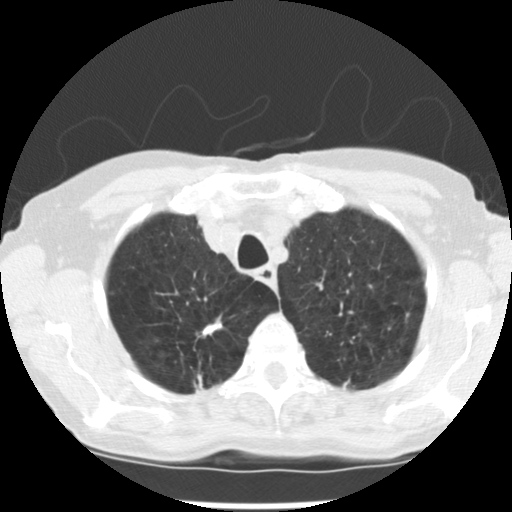
Low-dose screening chest CT, axial slice; first (baseline) screen; lung window (W 1500 / L -600 HU); 2.5 mm slice thickness; standard (soft-tissue) reconstruction kernel (STANDARD); 120 kVp; slice 39 of 265 in the series. Female participant, aged 72 years at enrolment. Current smoker at enrolment.
Lesion marked by an expert reader, bounding box (x1, y1, x2, y2) in pixels: (184, 311, 232, 349). The screening reader recorded 3 non-calcified nodules or masses ≥4 mm on this exam; which of them this box marks is not recorded. Participant outcome: lung cancer diagnosed 50 days after this screen — adenocarcinoma, NOS, right upper lobe, moderately differentiated (G2), stage IB (AJCC 6th edition), 22 mm at pathology.